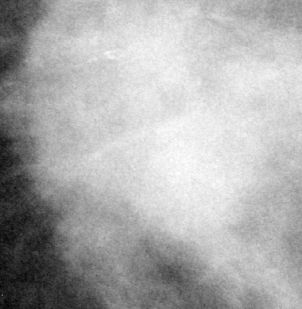
Region of interest cut from a scanned film mammogram (one marked finding), left breast, CC view, BI-RADS breast density category 3 (scale 1–4).
Mass, shape irregular / architectural distortion, margins ill defined / spiculated; BI-RADS assessment category 4; subtlety rating 4 on a 1 (subtle) to 5 (obvious) scale; pathology result (as recorded, not read from the image): malignant.